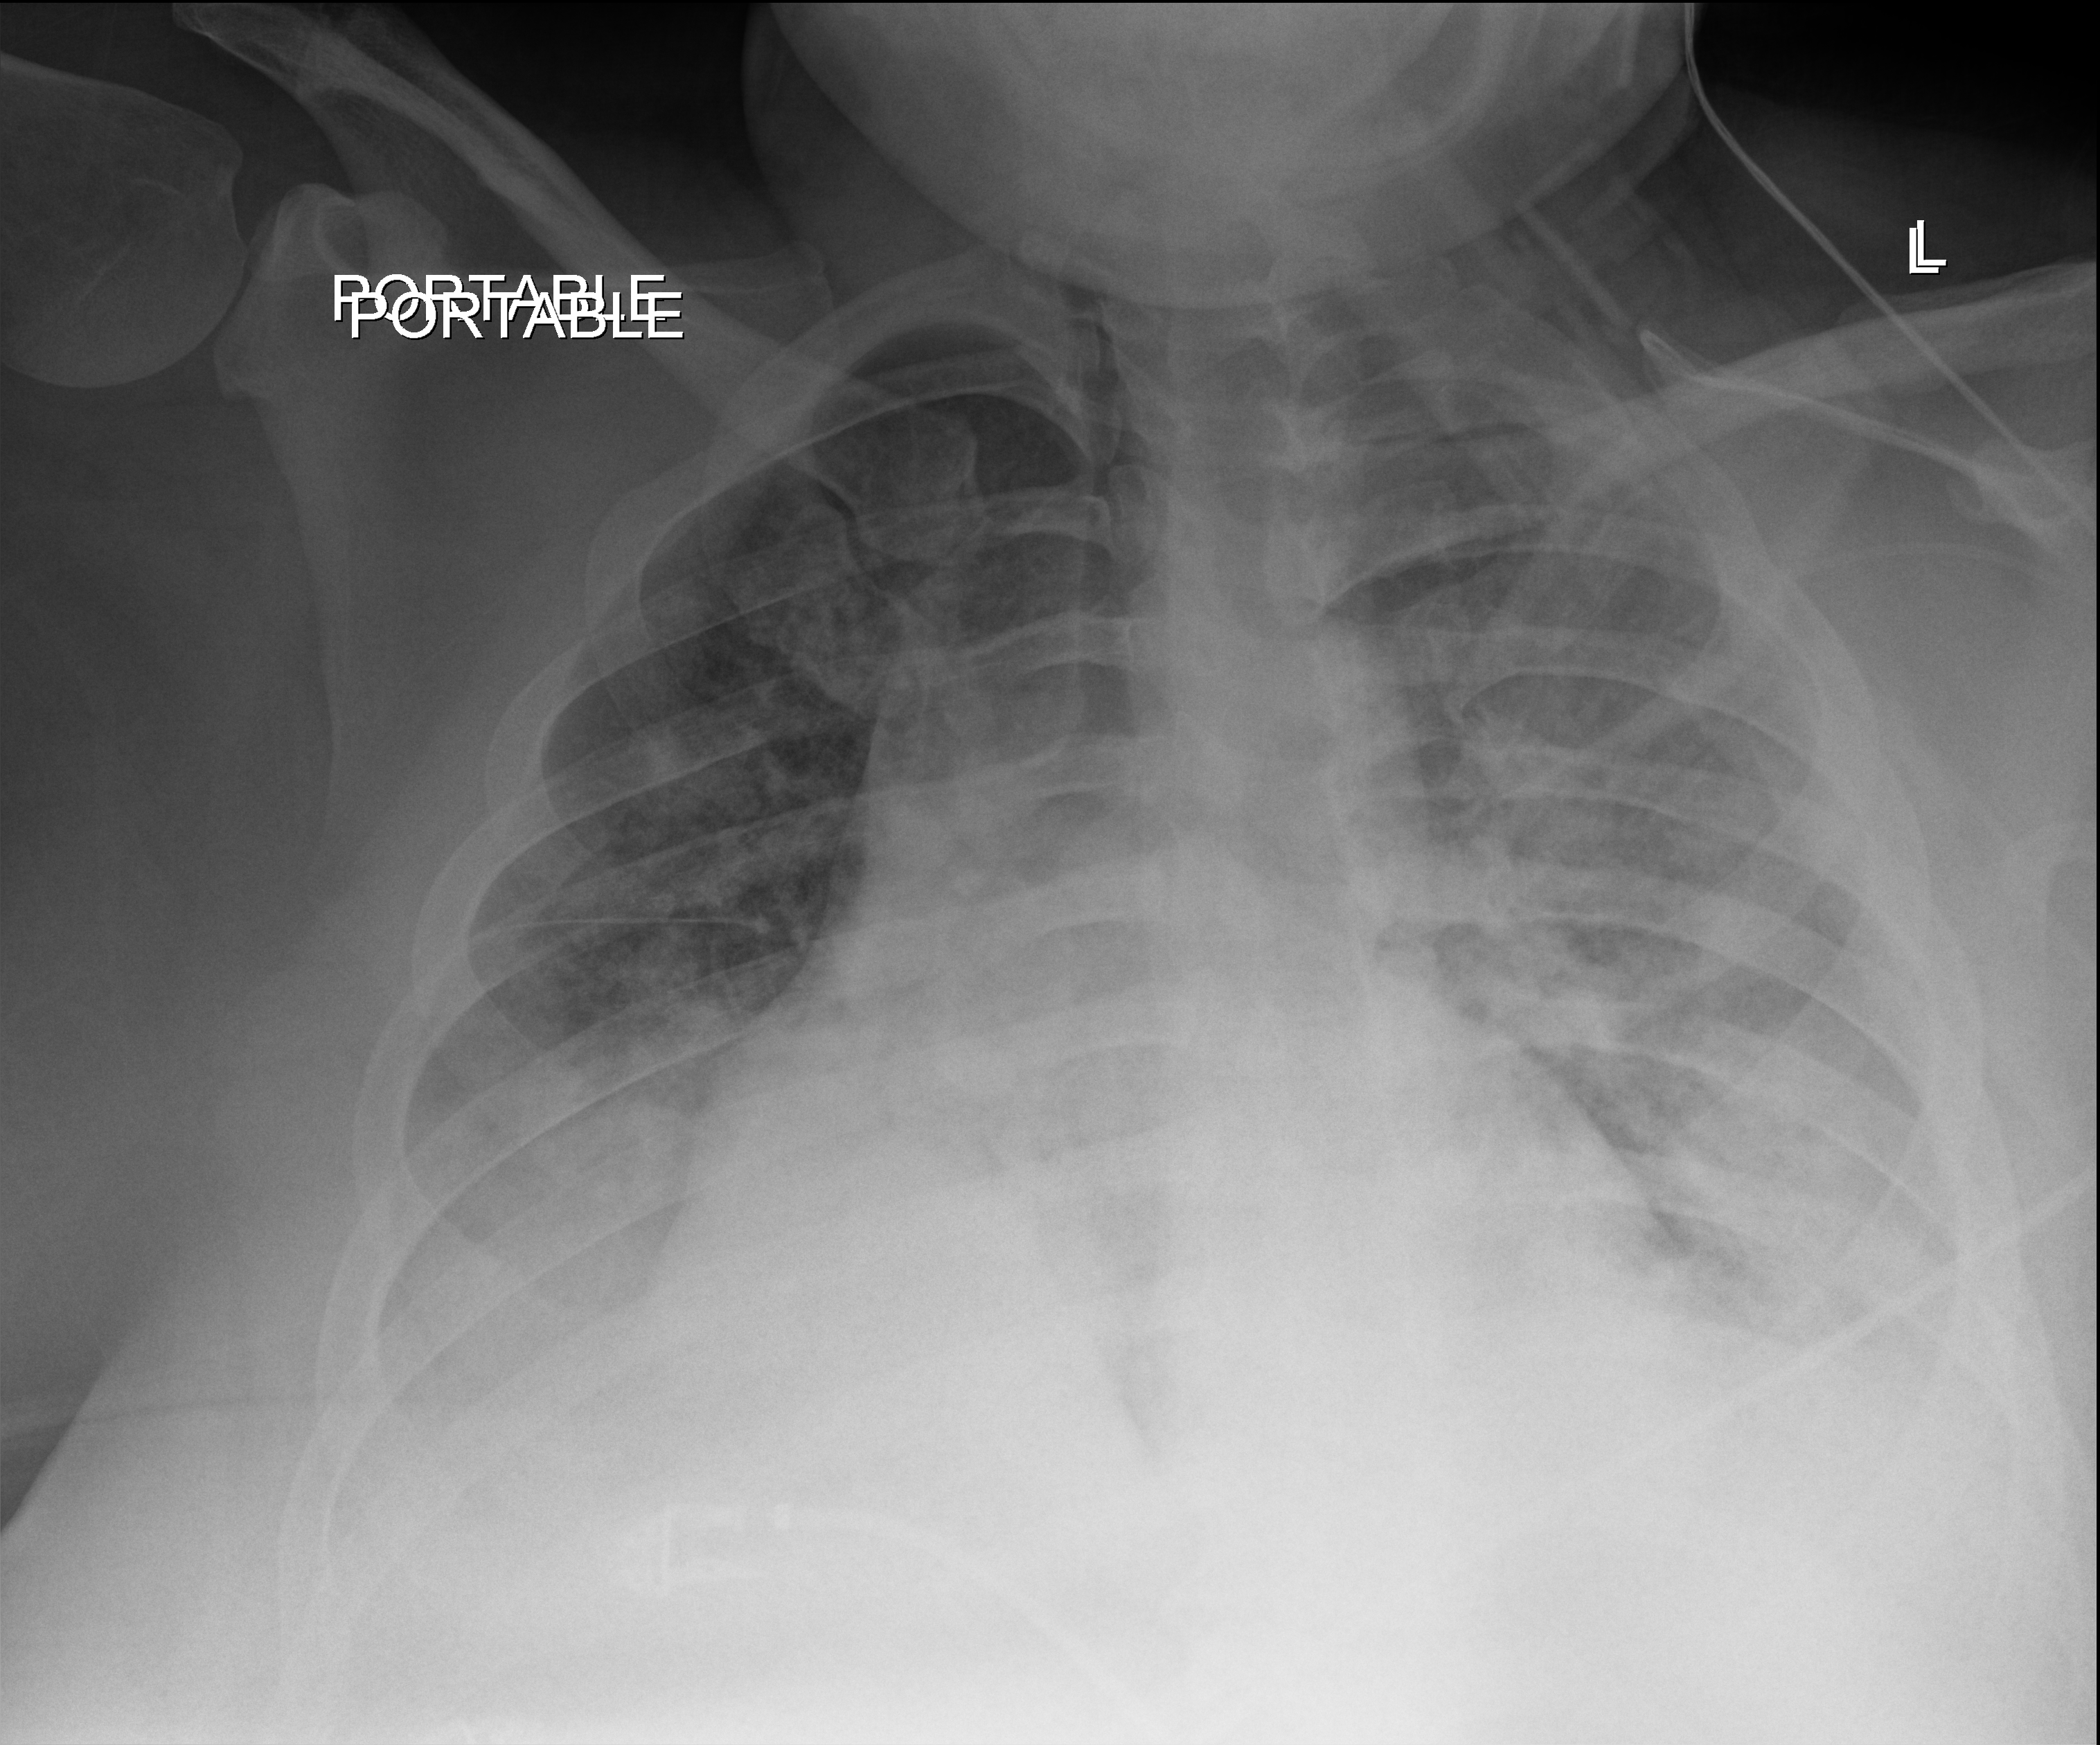
Chest radiograph (digital radiography); anteroposterior (AP) projection. Male patient hospitalised with COVID-19, age 18–59 years.
From the hospital-stay record, not from the radiograph (when in the stay this image was taken is not recorded):
- admitted to intensive care during this hospital stay: yes
- mechanically ventilated during this hospital stay: no